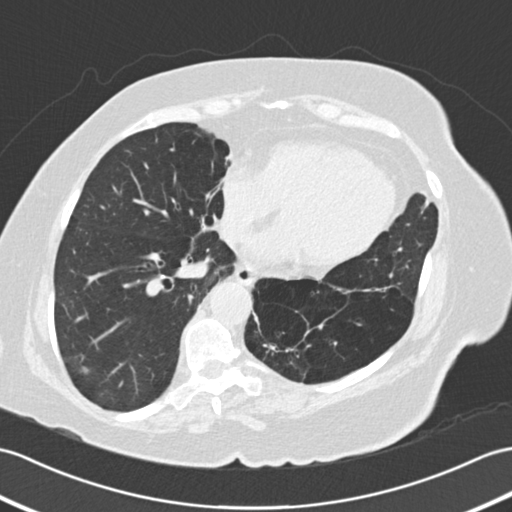
Low-dose screening chest CT, one axial slice. Slice 65 of 161 in the series (ordered by position). Reconstruction kernel B30f. 120 kVp. Lung window (W 1500 / L -600 HU). 2 mm slice thickness. 512 × 512 image matrix, field of view 353 × 353 mm.
Outlined on this slice (expert manual segmentation):
- lesion 1 (tumor, lower lobe of right lung): box from (x=84, y=368) to (x=88, y=372) px